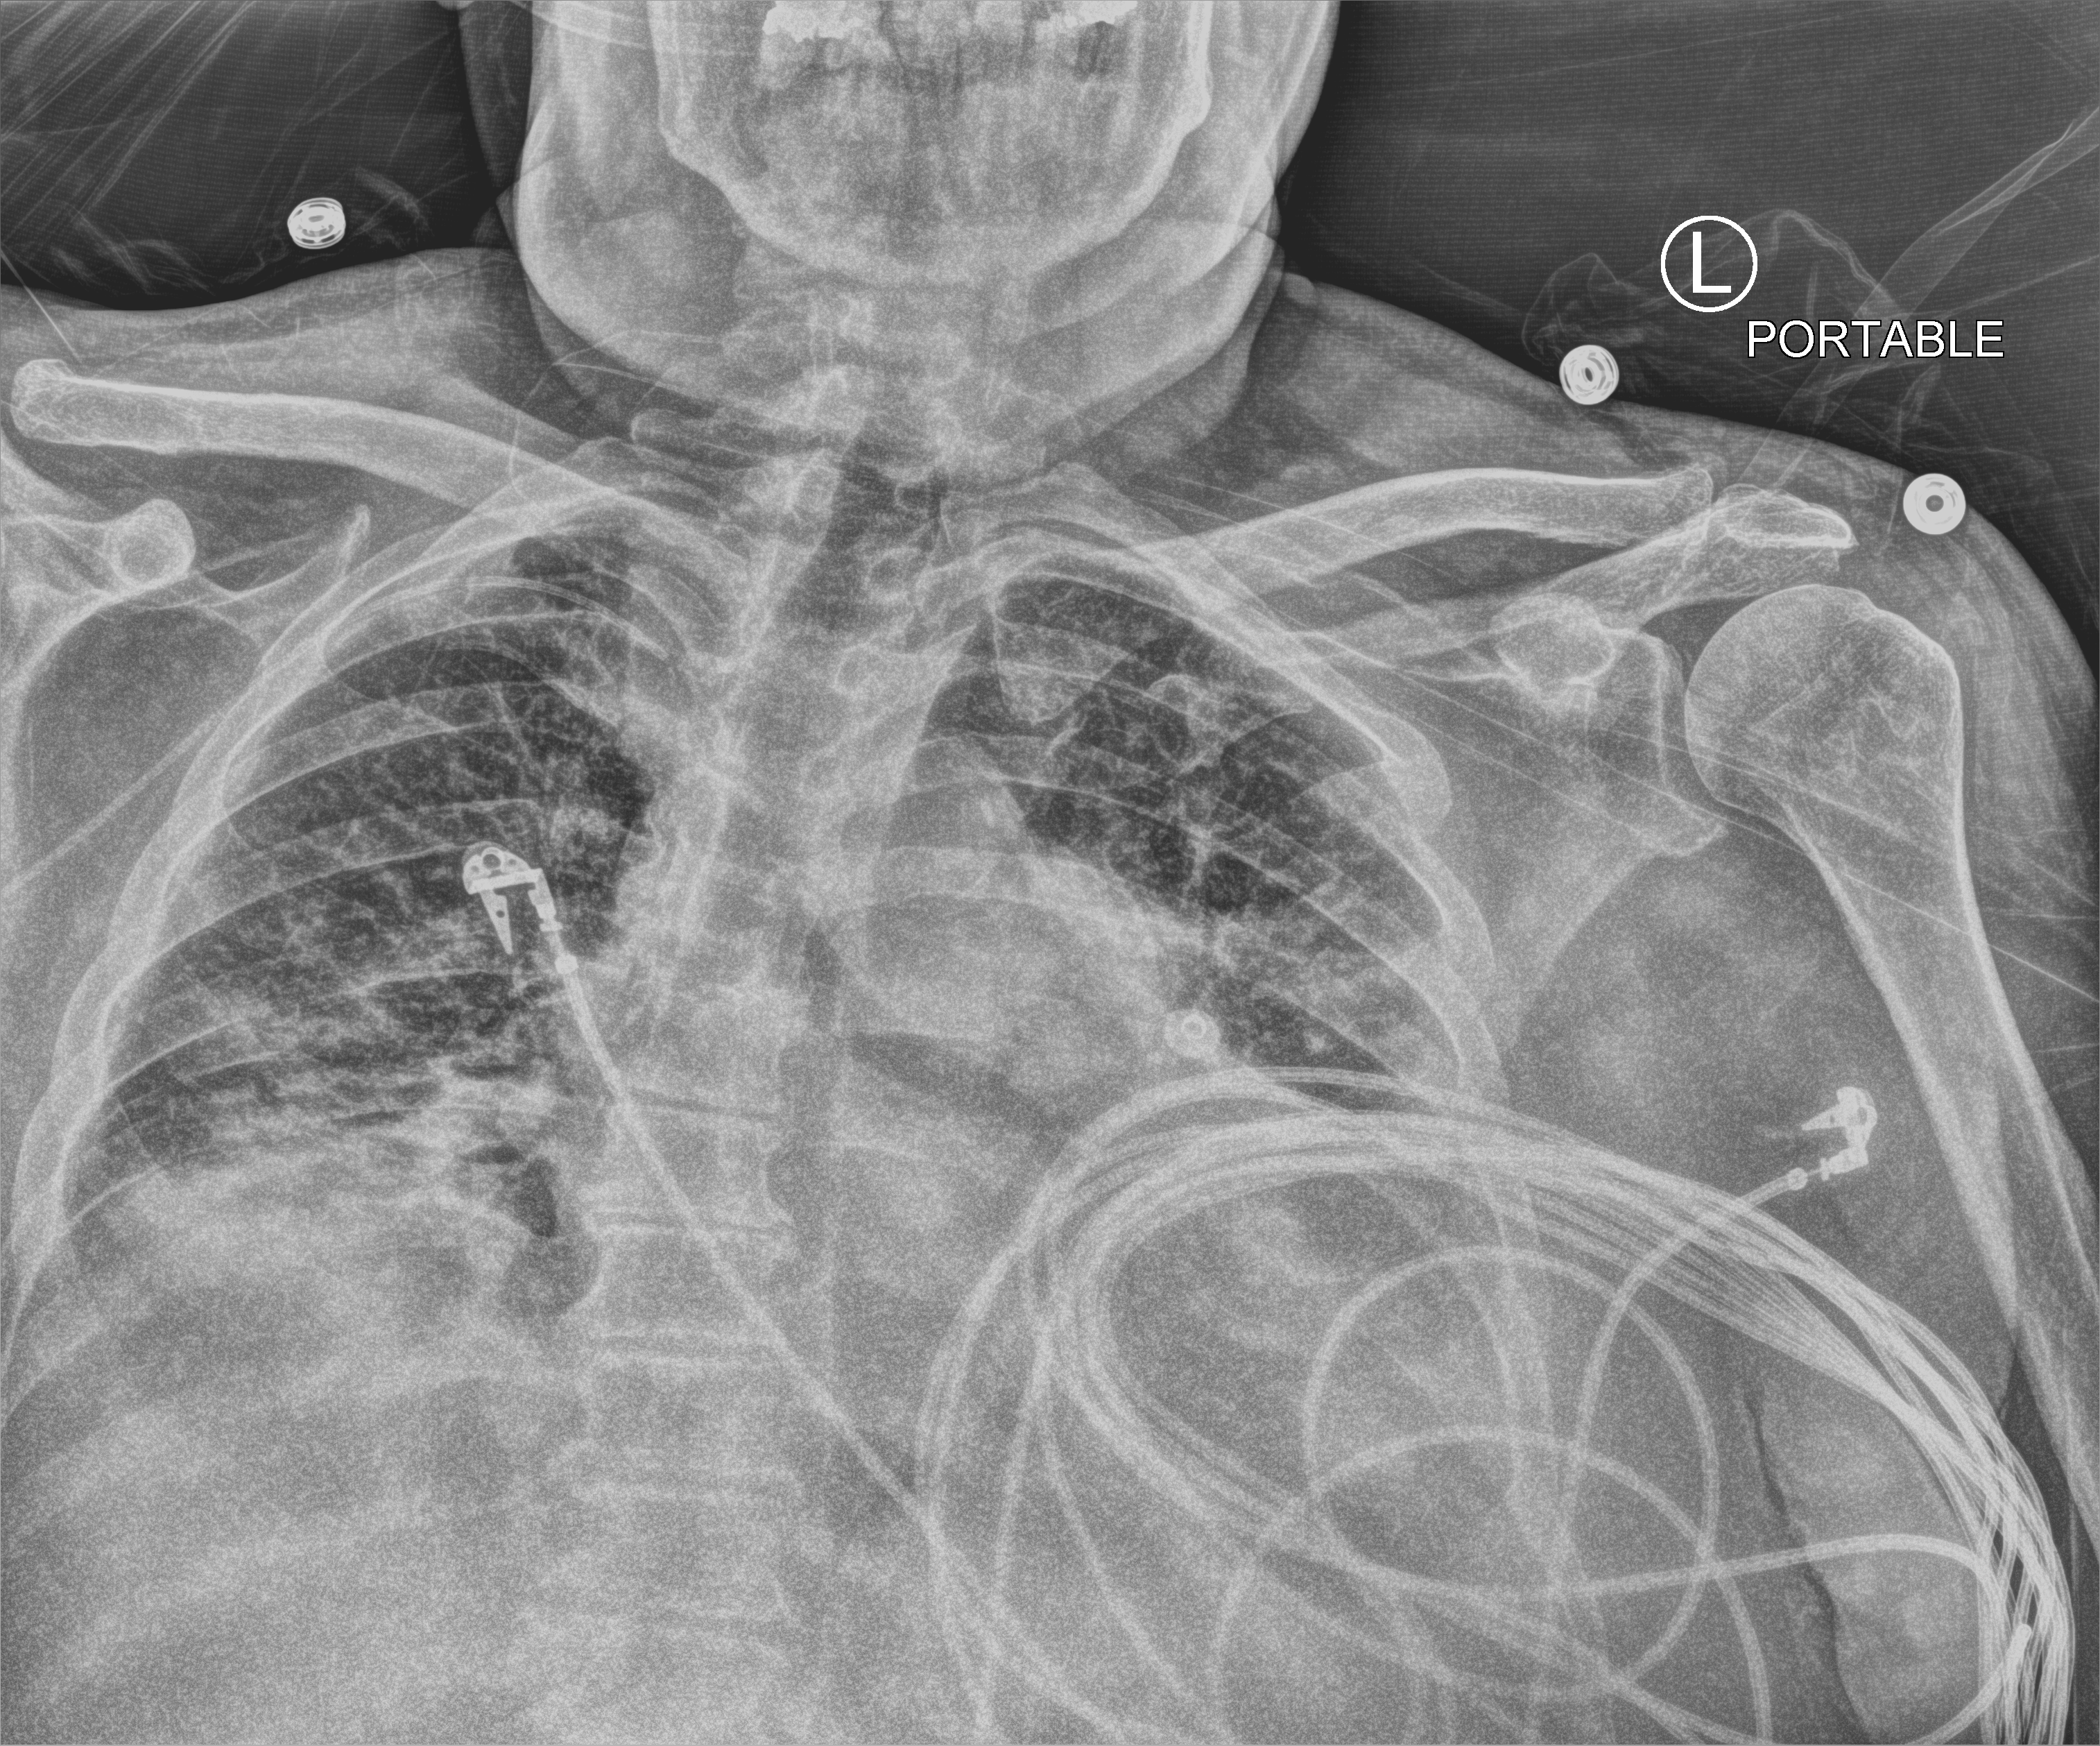
Portable chest radiograph. Male patient hospitalised with COVID-19, age 60–74 years.
Admission-level facts for this patient (not findings on this image; timing relative to this image not recorded): mechanically ventilated during this hospital stay: yes.